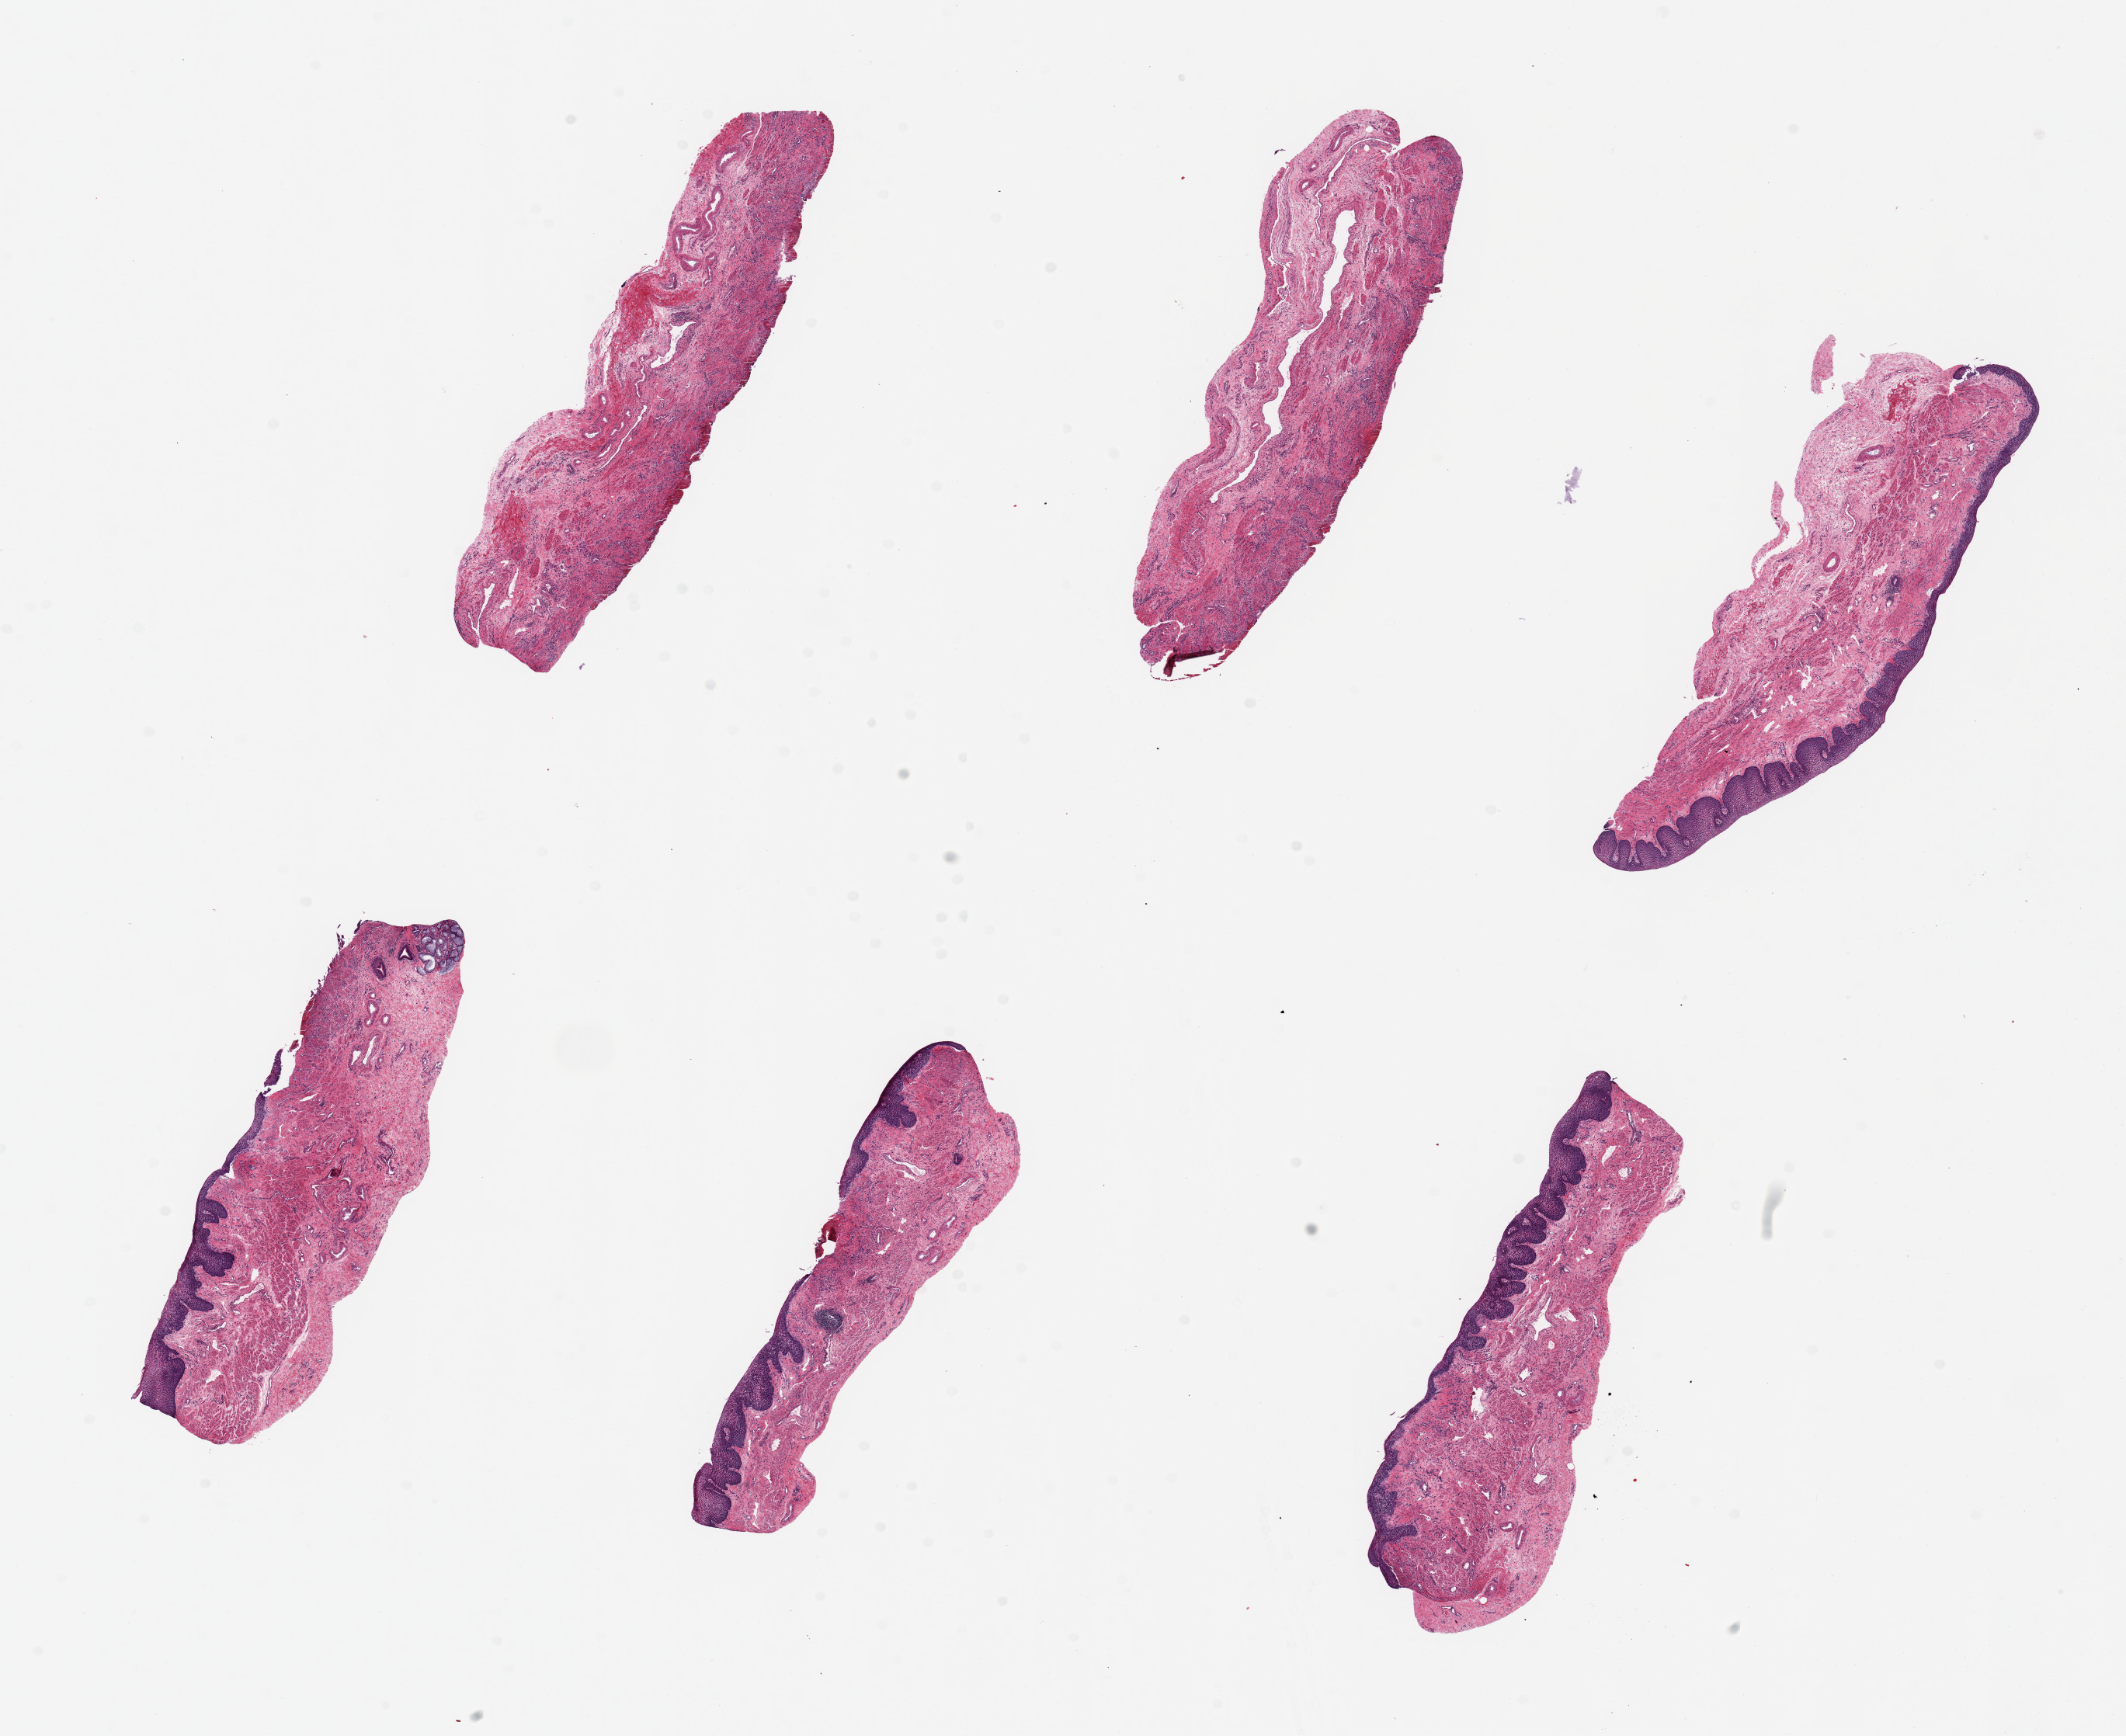
Digitized haematoxylin and eosin-stained section, shown as a low-resolution overview of the whole scanned area (about 21.7 x 17.7 mm), PAXgene-fixed paraffin-embedded (PFPE) section, section of esophageal mucous membrane (target tissue), tissue donor sample. Donor: male.
Review note (as recorded): 6 pieces ~6x2mm, squamous mucosa ~10-15% thickness on 3 of 6, rest sloughed, chroniclly inflammed.